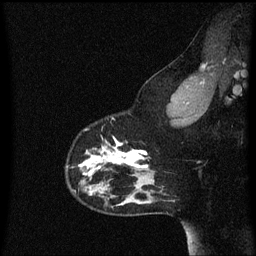
Breast MRI (dynamic contrast-enhanced), one sagittal slice. Position 47 of 60 along the scan axis. Dynamic contrast-enhanced series, image 2 of 3 at this slice position (ordered by acquisition). 1.5 T. TE 4.2 ms, TR 8.4 ms. 2 mm slice thickness. 256 × 256 image matrix, field of view 200 × 200 mm. Female patient, age 33 years.
Outlined on this slice (semi-automatically segmented with operator editing):
- analysis volume of interest (the breast-tissue region the enhancement analysis was run in; not a lesion): bounding box [x1, y1, x2, y2] px = [66, 116, 152, 191]
- tumour enhancement mask (voxels above the 70 % enhancement threshold inside the analysis volume of interest): [80, 136, 149, 177]